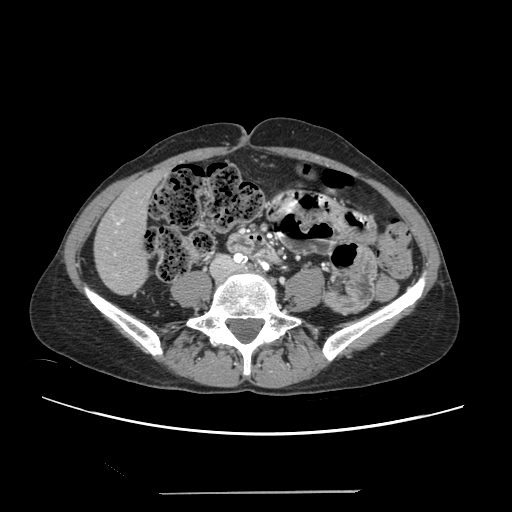
Contrast-enhanced abdominal CT, one axial slice; 120 kVp; intravenous contrast given; soft-tissue window (W 400 / L 40 HU); 512 × 512 image matrix. Female patient, age 60 years. From the clinical record (not read from this slice): diagnosis: colorectal cancer liver metastases, imaged before liver resection; multiple liver metastases: no; largest metastasis: 1.5 cm; disease in both lobes: no.
Annotated regions visible in this slice (manually delineated by an expert):
- liver: bounding box <95,174,161,294> (left, top, right, bottom; pixels)
- planned liver remnant (the part of the liver to remain after resection): <95,174,161,294>
- portal vein (with intrahepatic branches): <107,215,124,275>